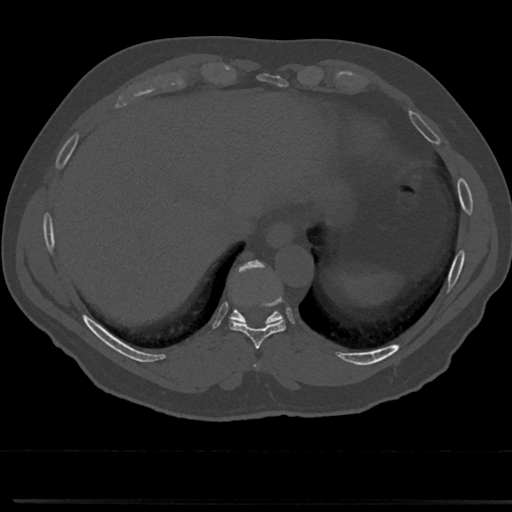
CT including the spine, one axial slice; slice 290 of 817 in the series (ordered by position); reconstruction kernel Br40s/3; bone window (W 1800 / L 400 HU); 512 × 512 image matrix, field of view 355 × 355 mm. Male patient, age 61 years. Case-level facts recorded for this patient, not image findings: primary cancer: prostate.
Structures marked on this image (semi-automatically segmented with operator editing):
- T8 vertebra: box from (x=255, y=342) to (x=264, y=371) px
- T9 vertebra: (x=212, y=265)–(x=302, y=350)